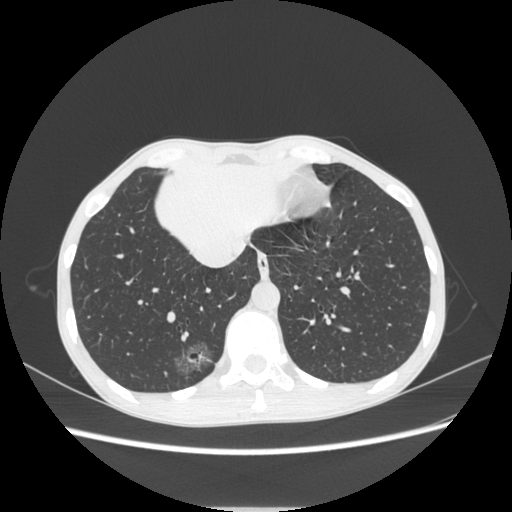
Chest CT, one axial slice. Slice 76 of 272 in the series (ordered by position). Reconstruction kernel STANDARD. Lung window (W 1500 / L -600 HU). 1.25 mm slice thickness. 512 × 512 image matrix, field of view 350 × 350 mm. Female patient, age 51 years. Case-level facts recorded for this patient, not image findings: clinical TNM (as recorded): T1c N0 M0; histopathological grade: G2-3.
Annotated regions visible in this slice (bounding box drawn by a radiologist):
- lung tumour (recorded histology: adenocarcinoma): box from (x=168, y=330) to (x=219, y=386) px